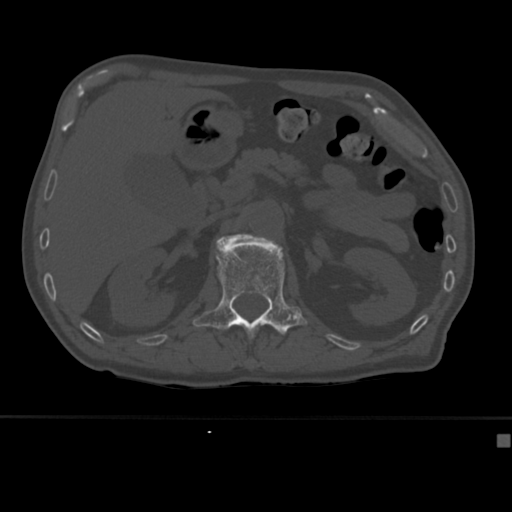
CT including the spine, one axial slice. Slice 171 of 430 in the series (ordered by position). Reconstruction kernel Br40s. 120 kVp. Bone window (W 1800 / L 400 HU). 1.5 mm slice thickness. 512 × 512 image matrix, field of view 337 × 337 mm. Male patient, age 64 years. Case-level facts recorded for this patient, not image findings: primary cancer: uterus; vertebrae with lytic lesions (as recorded): T1, T4, T5, T7, L5.
Structures marked on this image (semi-automatically segmented with operator editing):
- L1 vertebra: bounding box (x1, y1, x2, y2) in pixels: (193, 233, 308, 338)